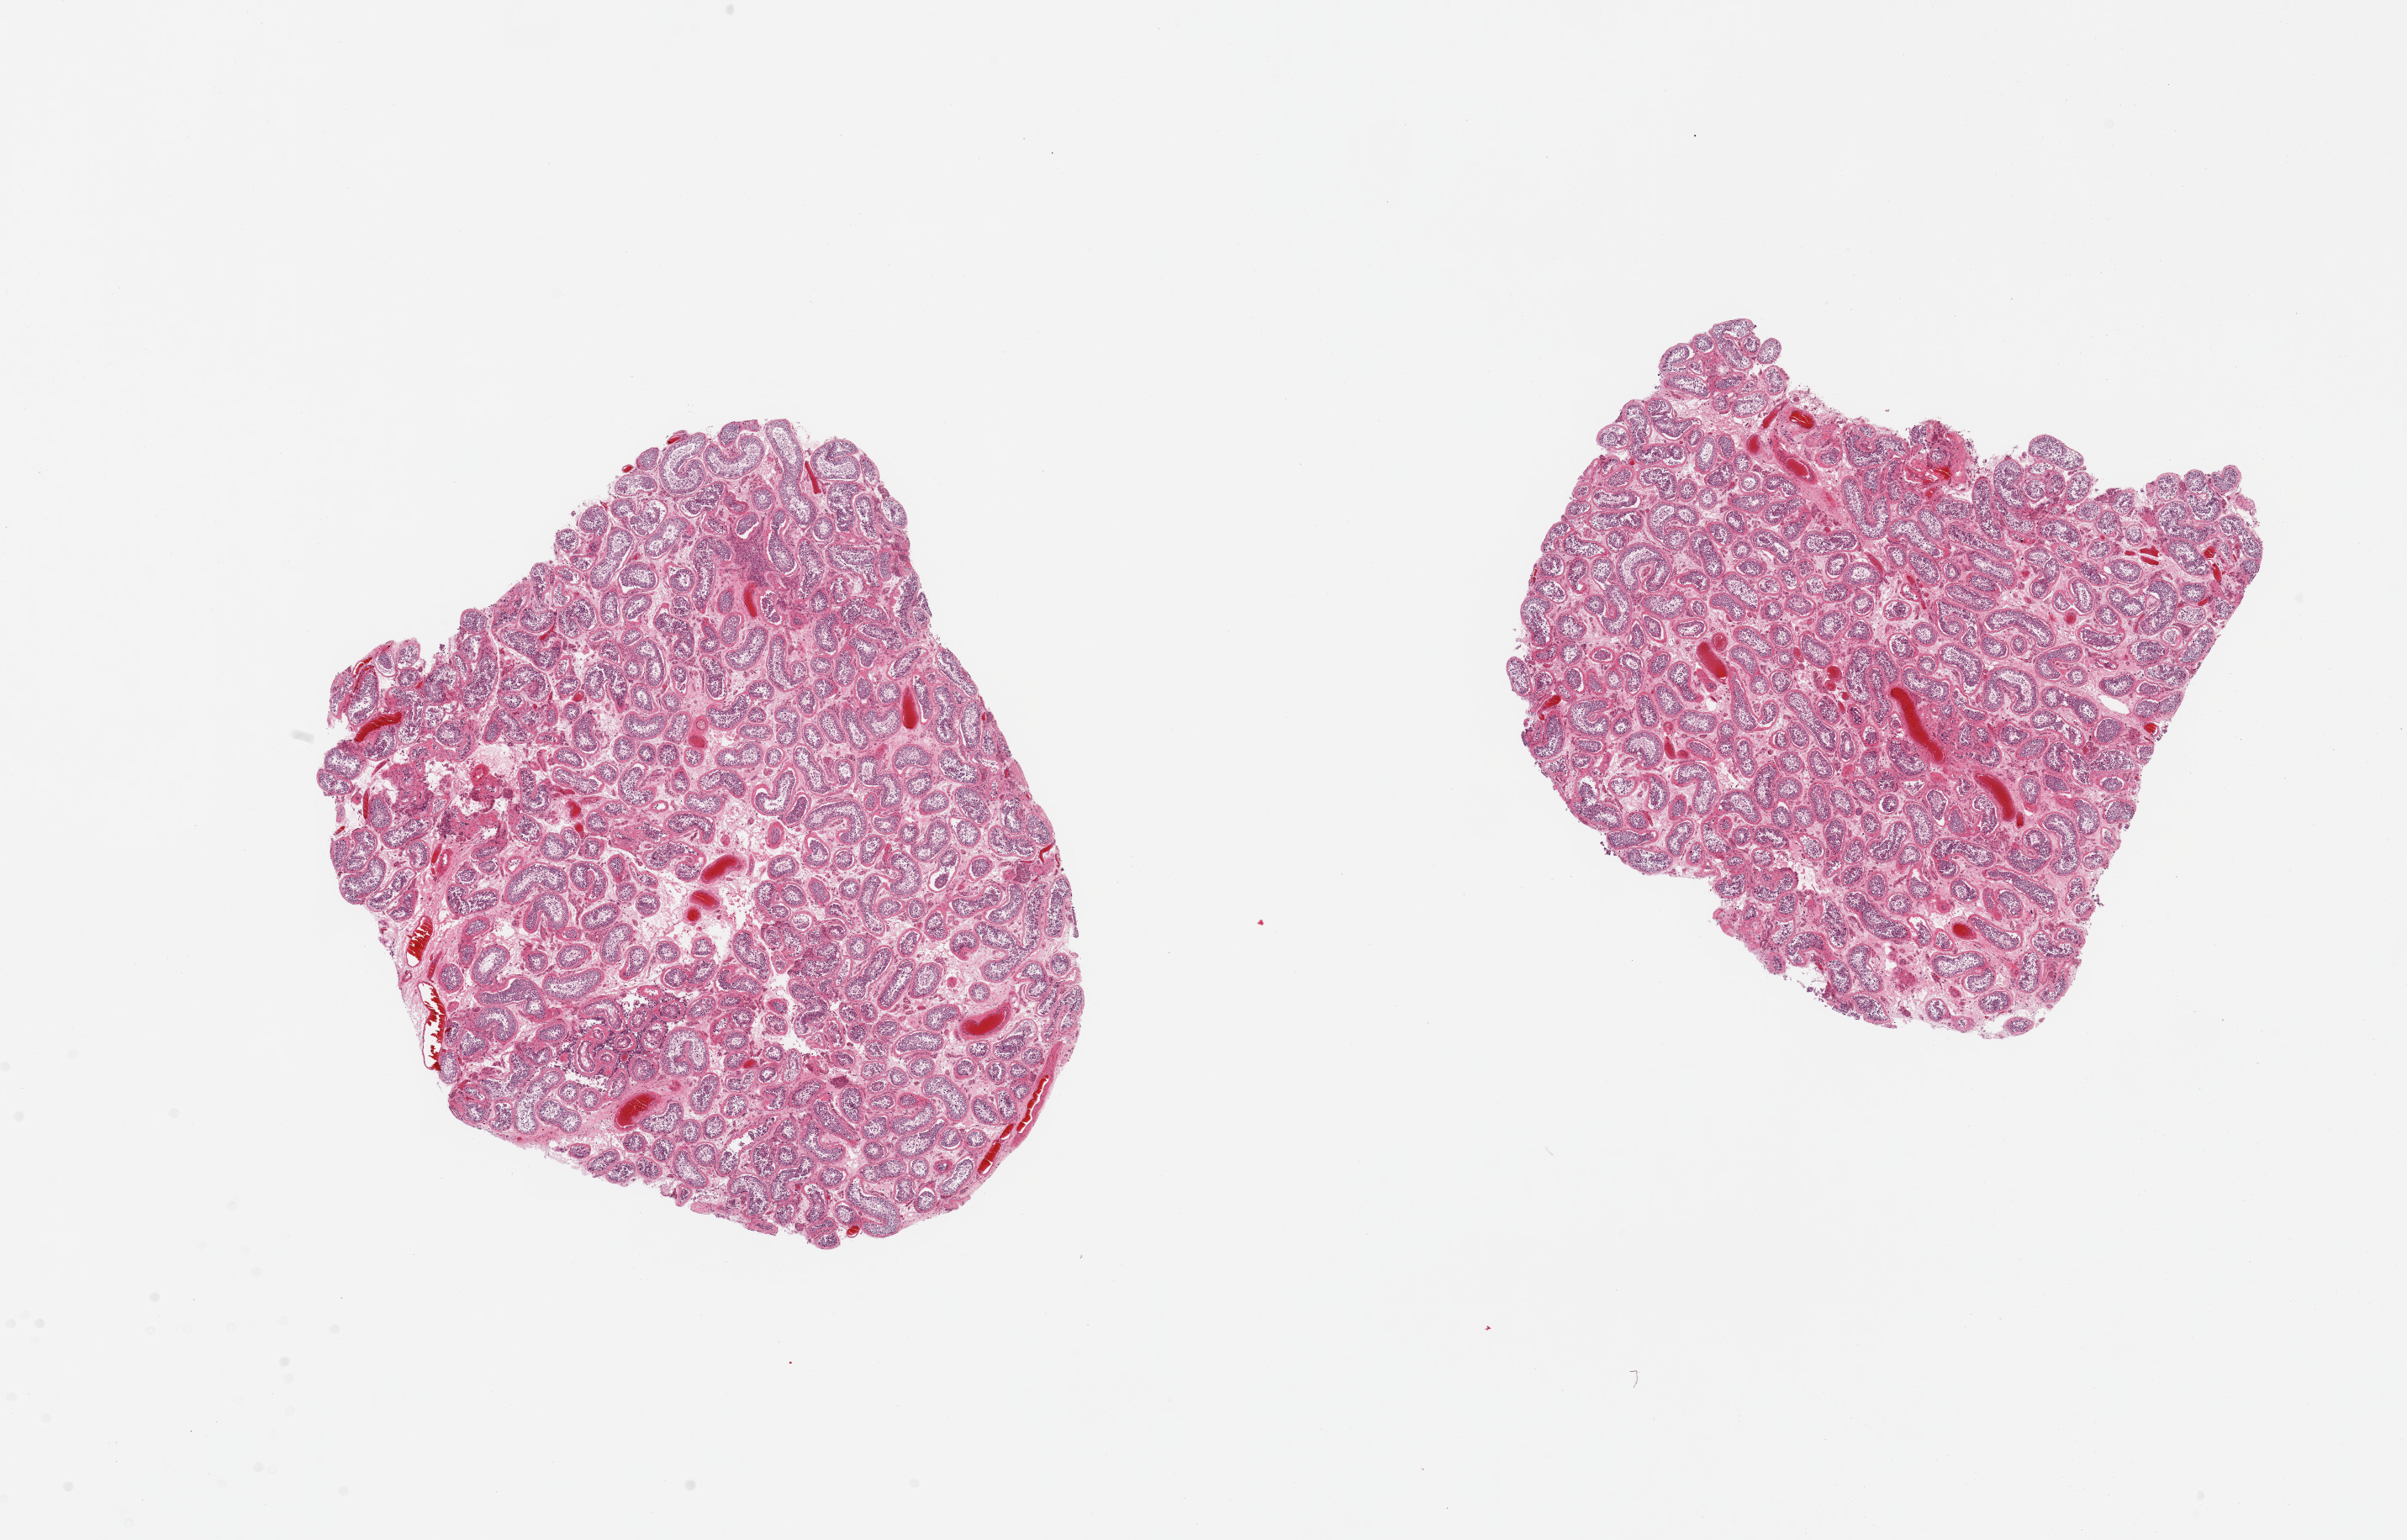
Haematoxylin and eosin whole-slide image, low-resolution overview of the scanned area, about 22.6 x 14.5 mm; PAXgene-fixed paraffin-embedded (PFPE) section; section of testis (target tissue); tissue donor sample. Donor: male.
Review note (as recorded): 2 pieces. spermatogenesis.